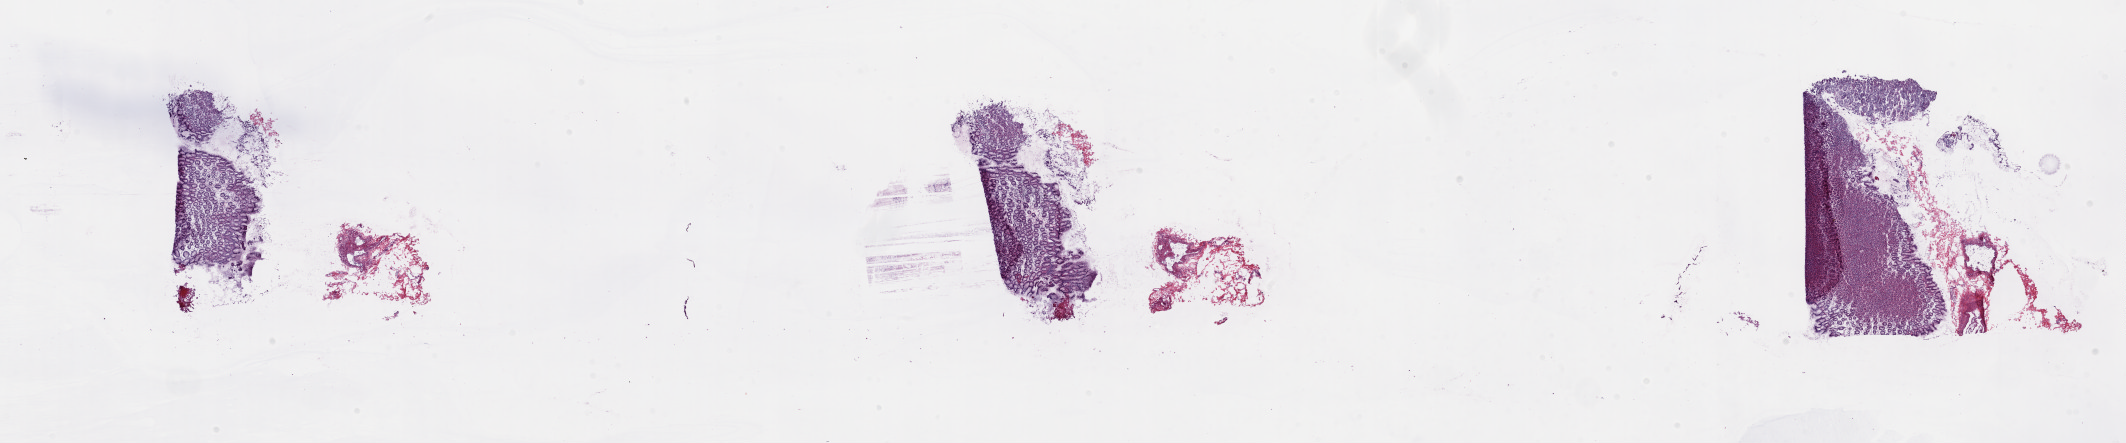
Whole-slide histology image, Hematoxylin and eosin (H&E) stained, shown as a low-resolution overview of the whole scanned area (about 33.7 x 7.0 mm), frozen section, solid tissue normal (non-tumour tissue) sample from the esophagus. Male patient; age at initial diagnosis 57 years.
This section: solid tissue normal sample (biorepository sample class). Patient diagnosis: Adenocarcinoma, NOS (lower third of esophagus).